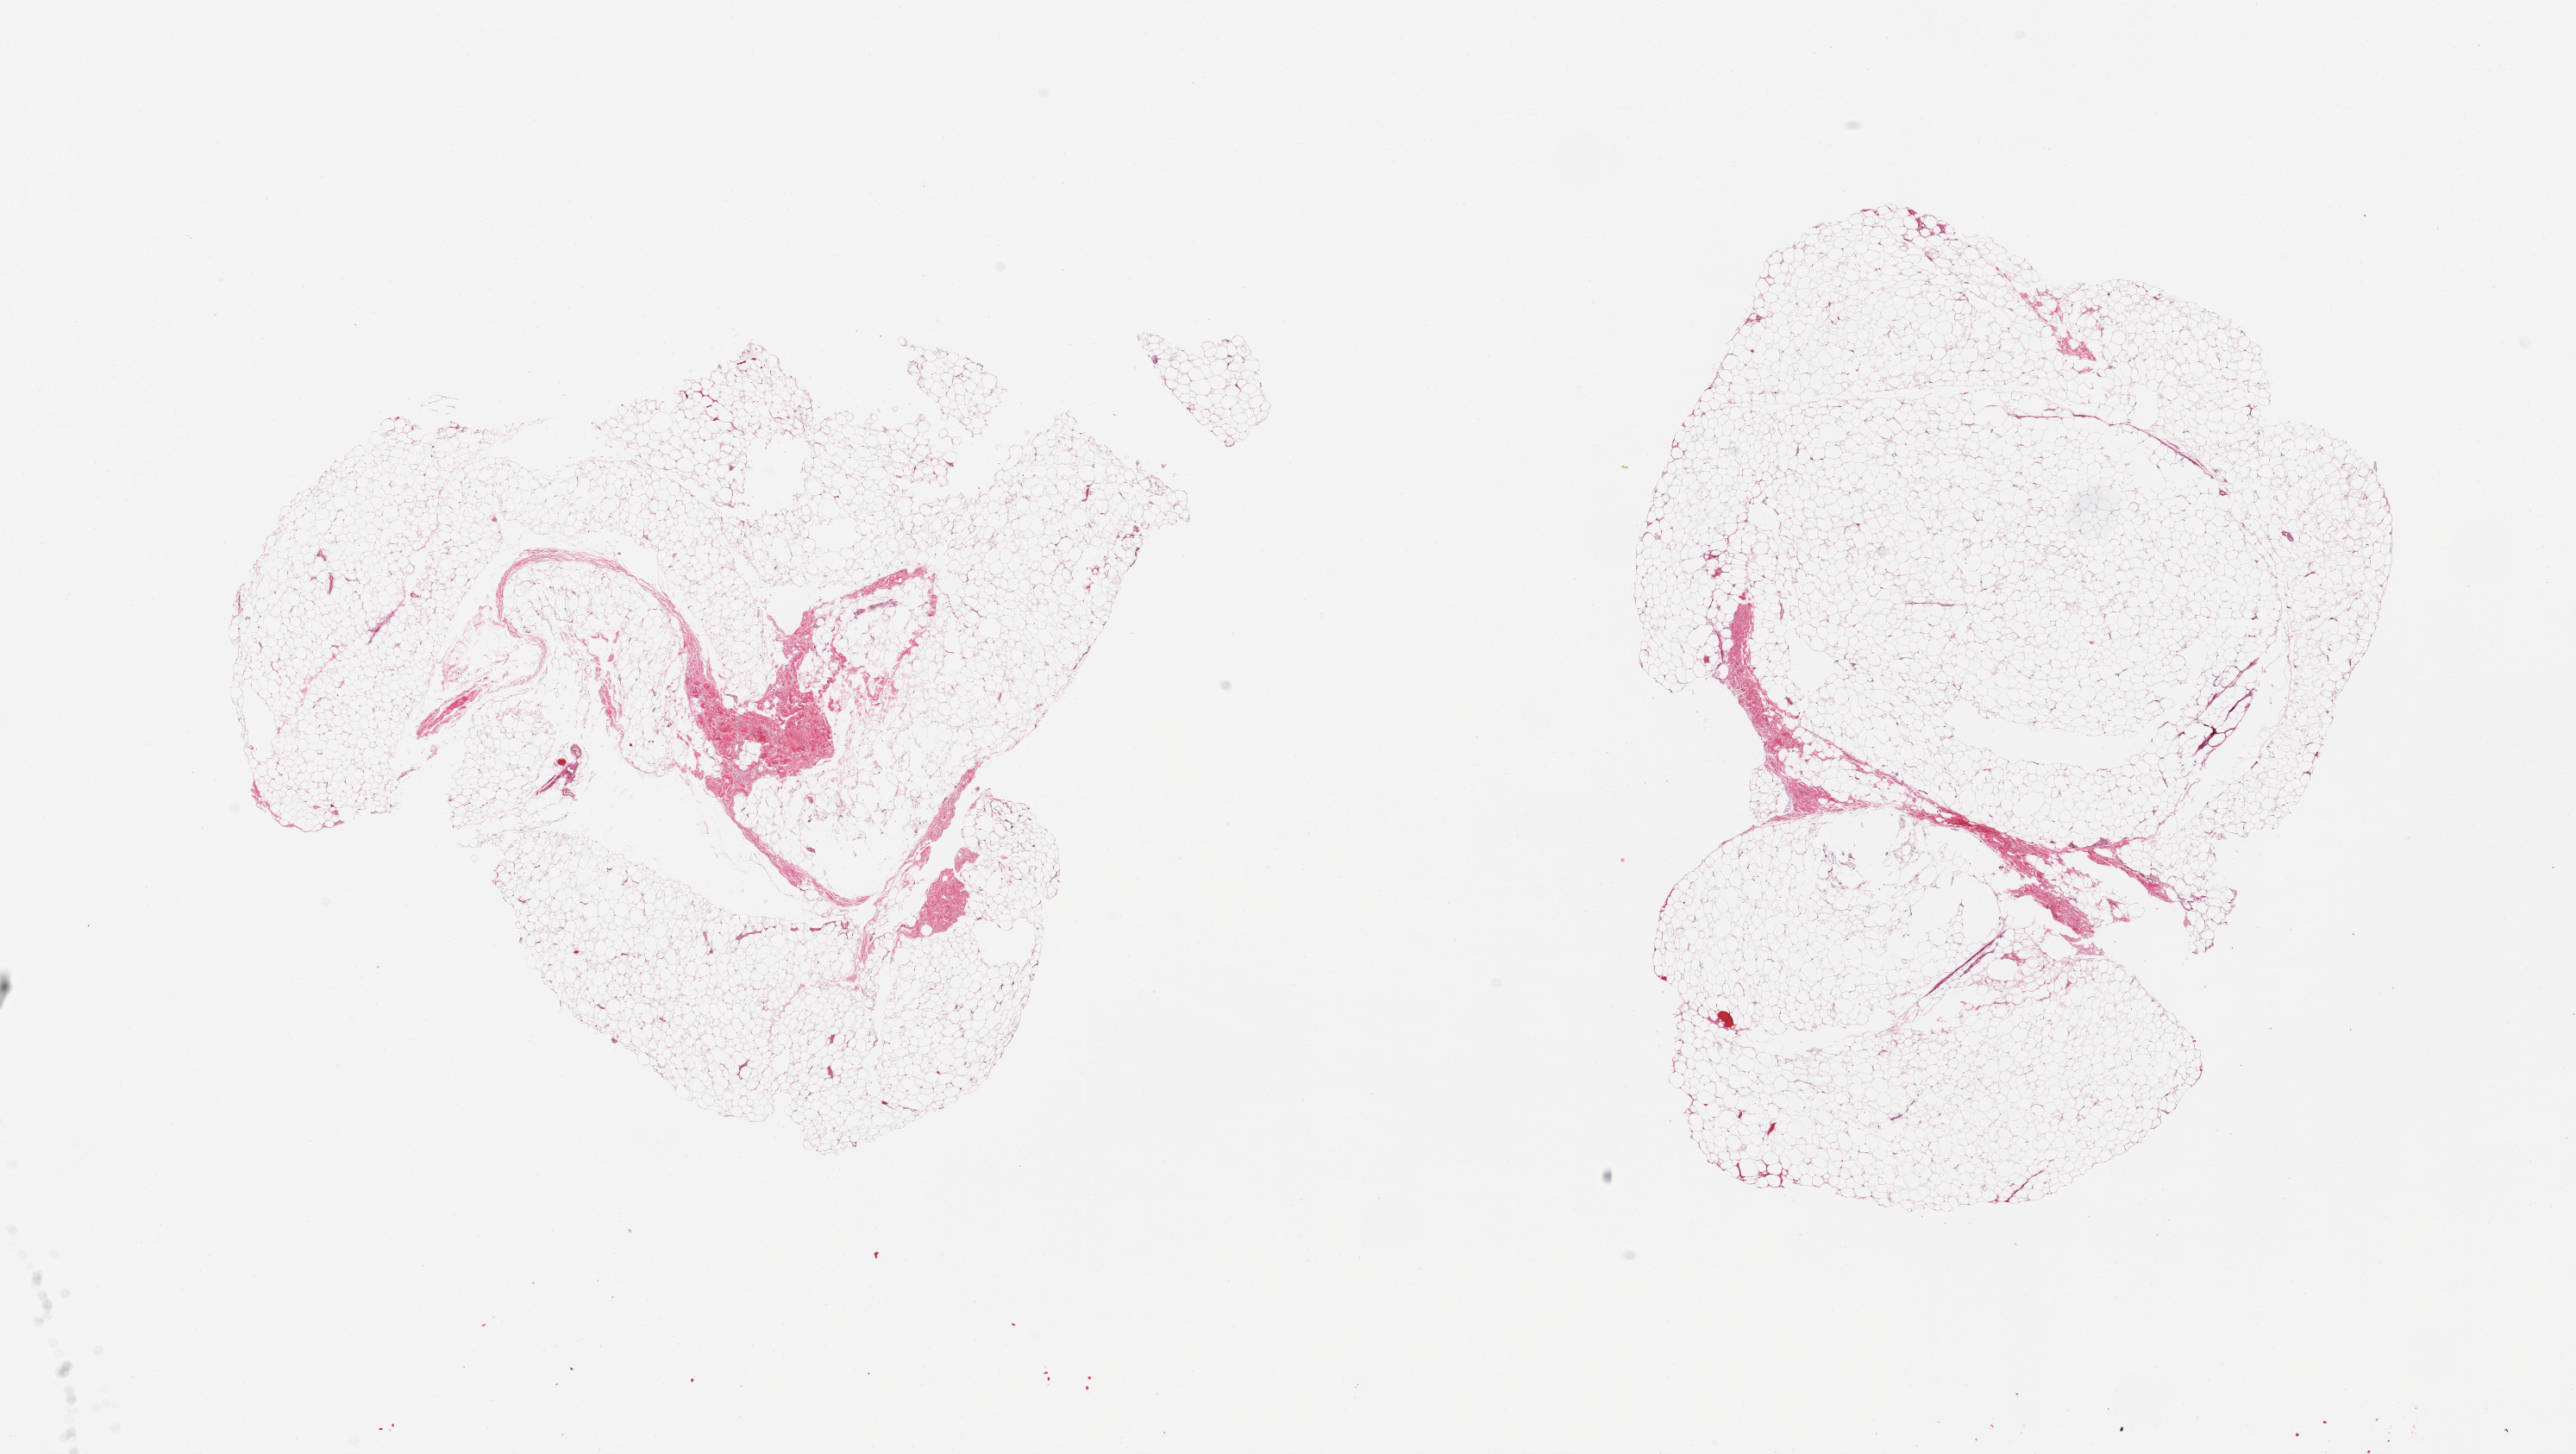
Digitized hematoxylin and eosin (H&E)-stained section, brightfield — whole scanned area (about 23.6 x 13.3 mm, acquisition: 20x scan) shown as a low-resolution overview. PAXgene-fixed paraffin-embedded (PFPE) section. Section of breast (target tissue). Donor tissue sample. Donor sex: male.
- pathologist's review note for this sample: 2 pieces, fibroadipose elements only